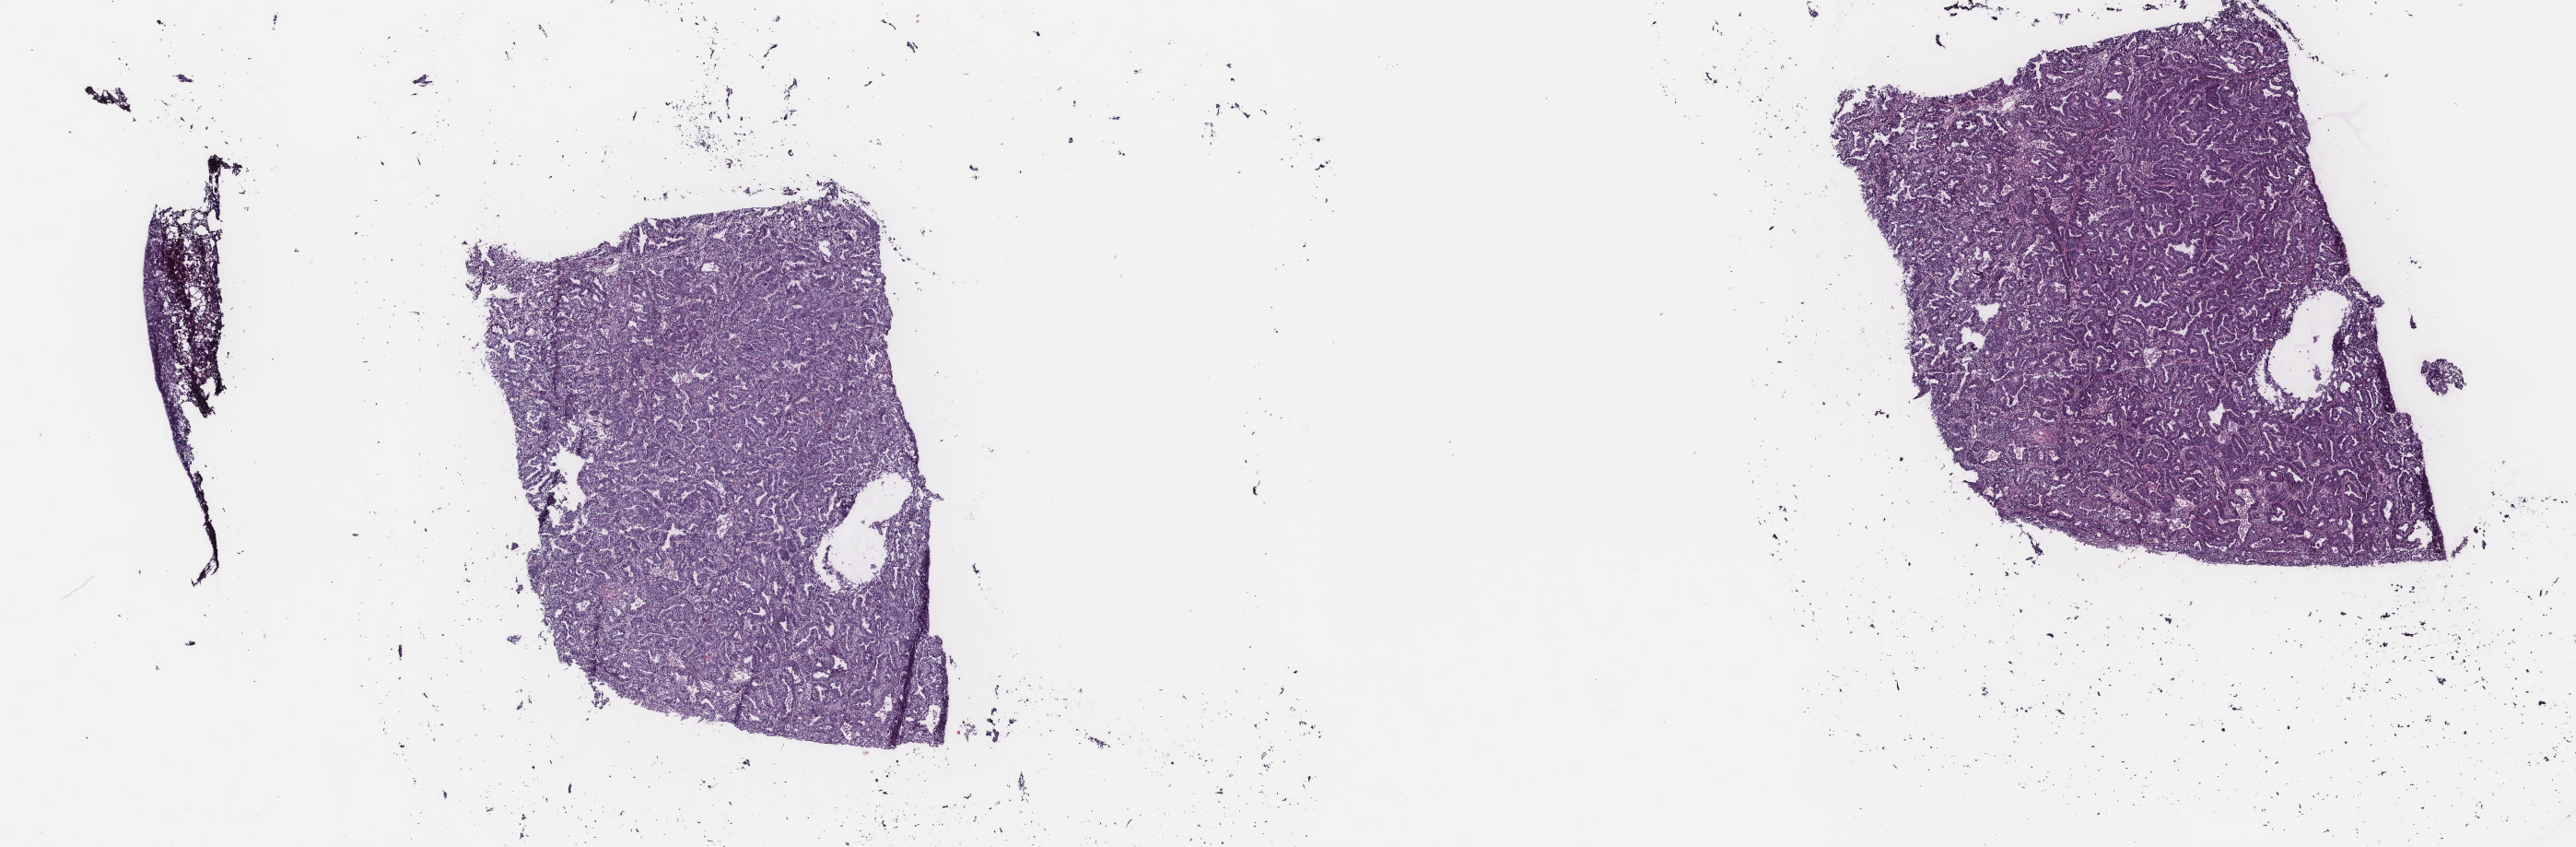
Whole-slide histology image, Hematoxylin and eosin (H&E) stained — whole scanned area (about 22.2 x 7.3 mm, acquisition: 40x scan) shown as a low-resolution overview. Frozen section. Uterus, primary tumour sample. Female, age 64 years at initial diagnosis. Histologic grade: G3 (poorly differentiated). Pathologist review of this section (percent, as recorded): tumour cells 90%, tumour nuclei 90%, normal cells 0%, stromal cells 5%, necrosis 5%. Infiltration values recorded for this section: lymphocyte infiltration 40%, monocyte infiltration 30%, neutrophil infiltration 20%.
Lymph nodes positive (case pathology): 0 of 28 examined. Diagnosis: Endometrioid adenocarcinoma, NOS (endometrium). FIGO stage: IC.